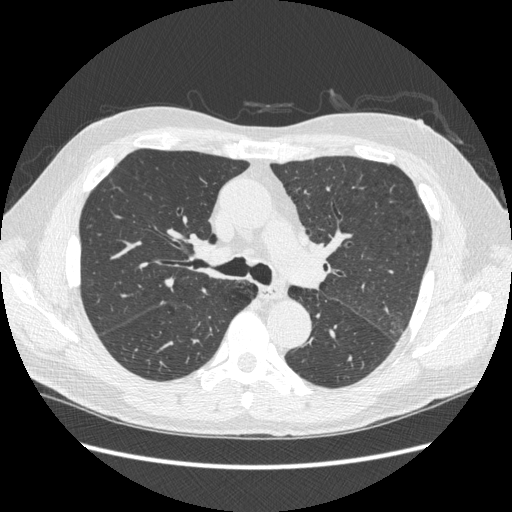
Chest CT (low-dose screening protocol), one axial image. Third screening round (two years after baseline). Lung window (W 1500 / L -600 HU). 1.25 mm slice thickness. Slice 101 of 258 in the series. Male participant, aged 59 years at enrolment.
- Lesion marked by an expert reader, box from (x=175, y=224) to (x=225, y=272) px.
- The screening reader recorded 2 non-calcified nodules or masses ≥4 mm on this exam (right upper lobe, left lower lobe); which of them this box marks is not recorded.
- Participant outcome: lung cancer diagnosed 169 days after this screen — squamous cell carcinoma, keratinizing, NOS, right hilum, stage IIIB (AJCC 6th edition).